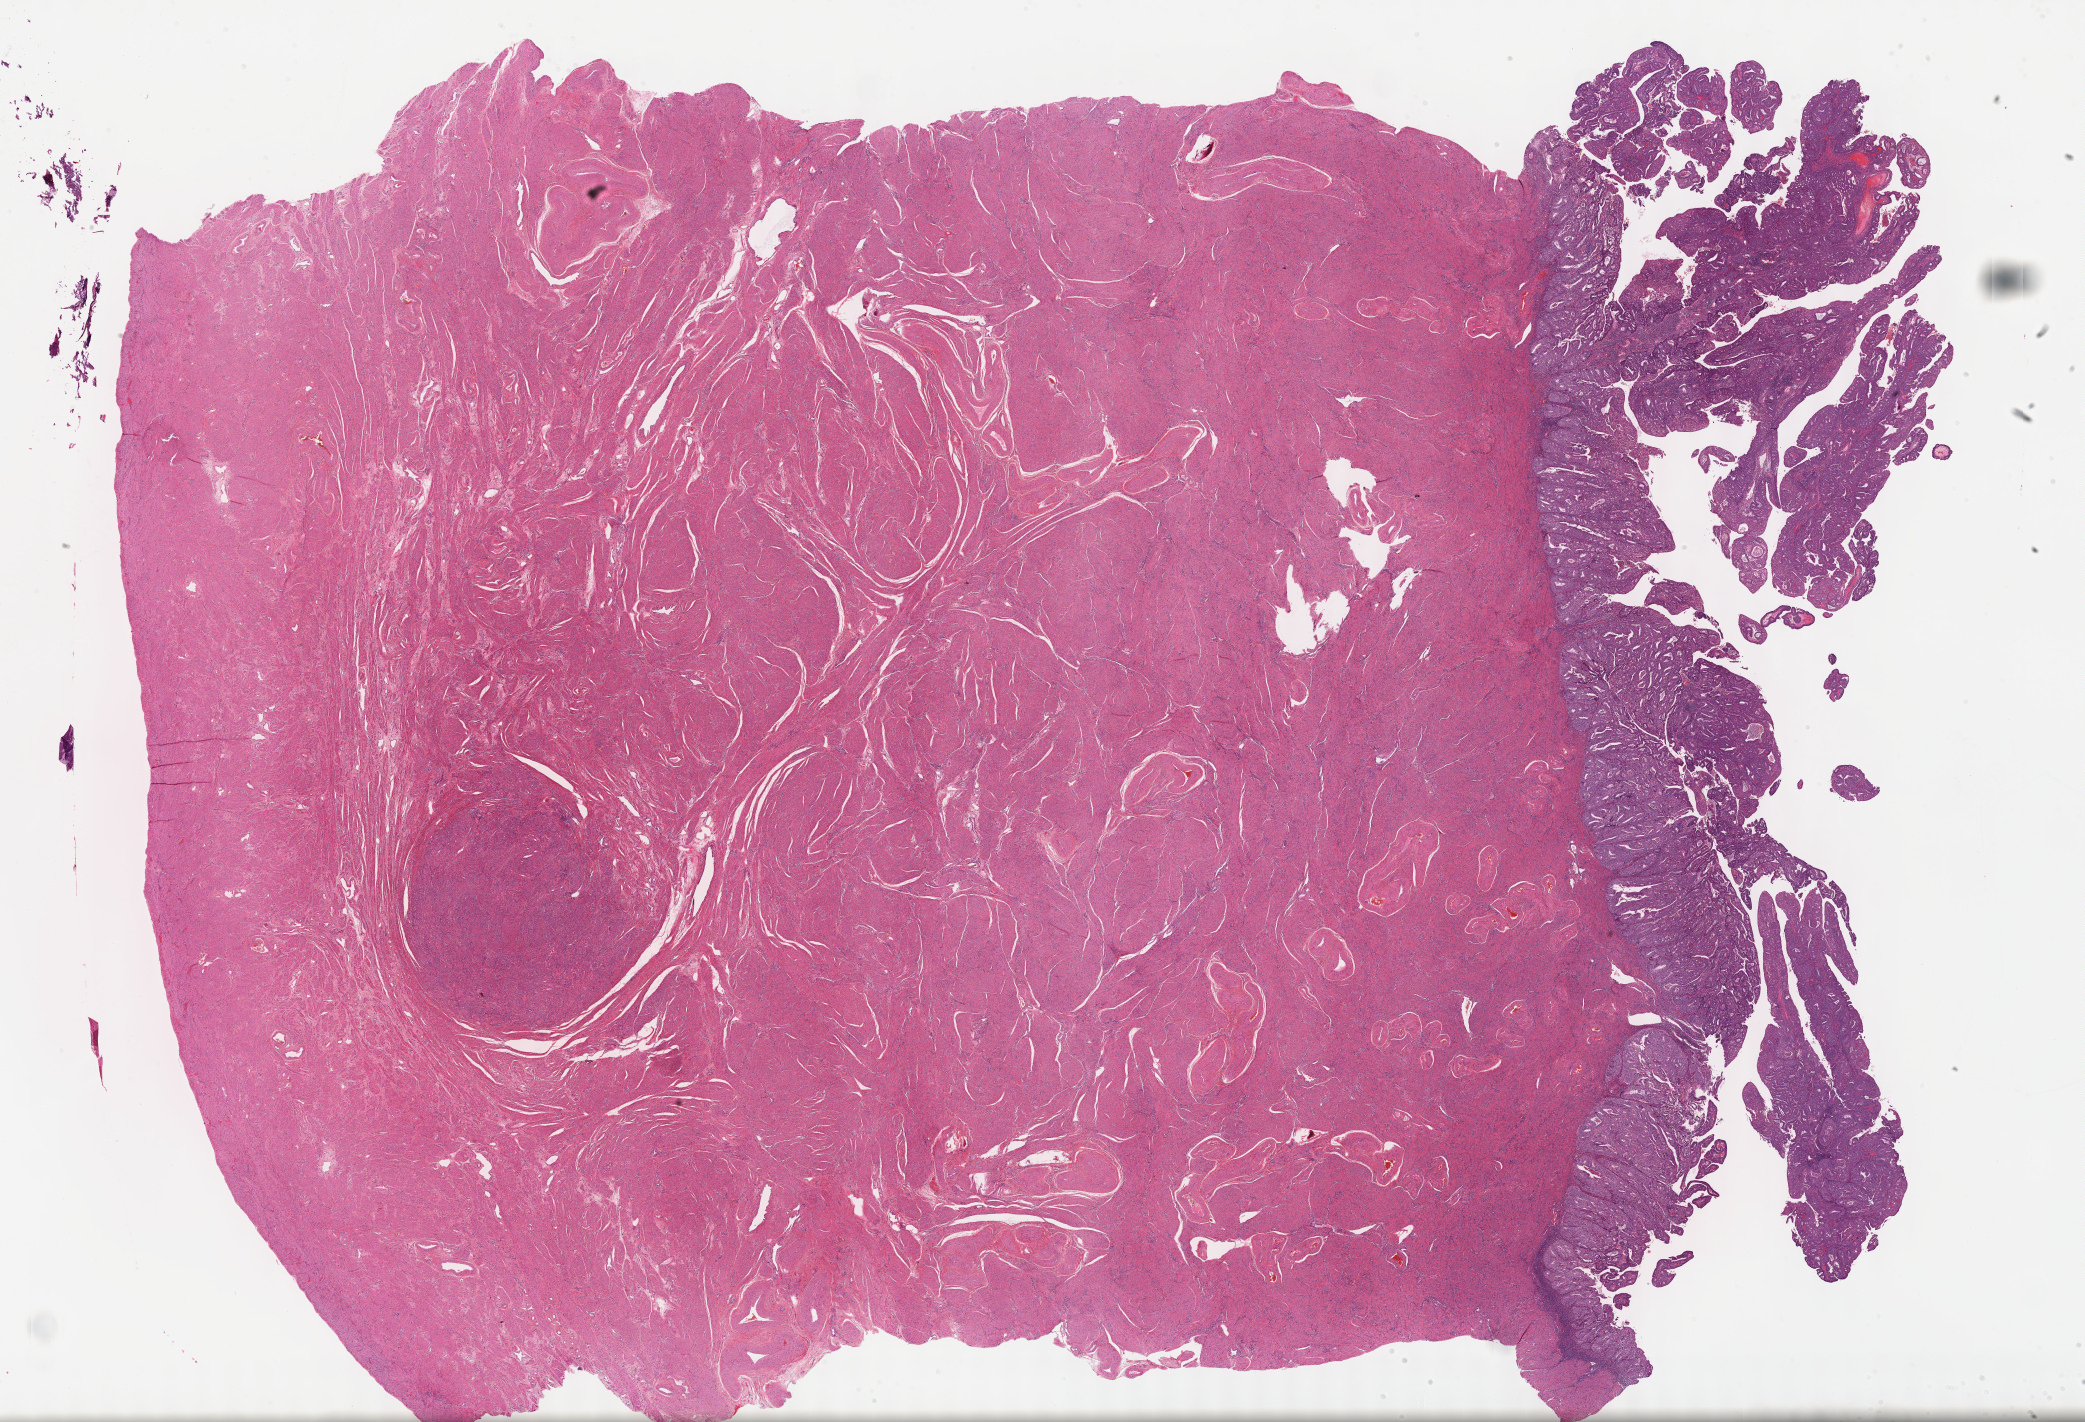
Digitized H&E tissue section (whole slide) — whole scanned area (about 33.7 x 23.0 mm, slide scanned at 40x) shown as a low-resolution overview, formalin-fixed paraffin-embedded (FFPE) diagnostic section, sample: primary tumour, uterus. Patient: female, age at initial diagnosis 38 years. Histologic grade: G2 (moderately differentiated).
• histologic diagnosis: Endometrioid adenocarcinoma, NOS (endometrium)
• lymph nodes positive (case pathology): 0 of 5 examined
• FIGO stage: IA